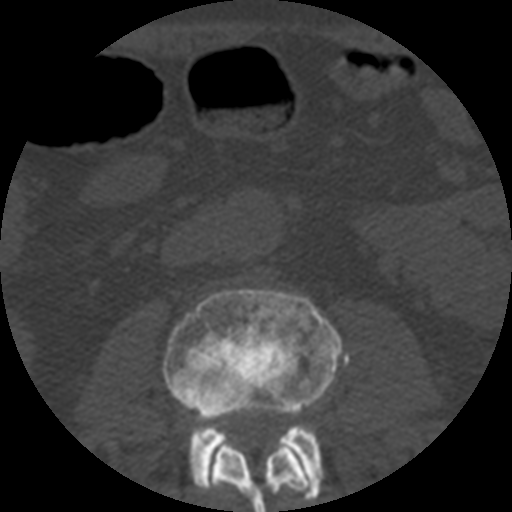
CT including the spine, one axial slice; slice 133 of 508 in the series (ordered by position); reconstruction kernel STANDARD; 120 kVp; bone window (W 1800 / L 400 HU); 512 × 512 image matrix, field of view 160 × 160 mm. Patient age 57 years. Case-level facts recorded for this patient, not image findings: primary cancer: prostate.
Outlined on this slice (semi-automatically segmented with operator editing):
- L2 vertebra: bounding box <202,431,314,512> (left, top, right, bottom; pixels)
- L3 vertebra: <163,289,349,501>